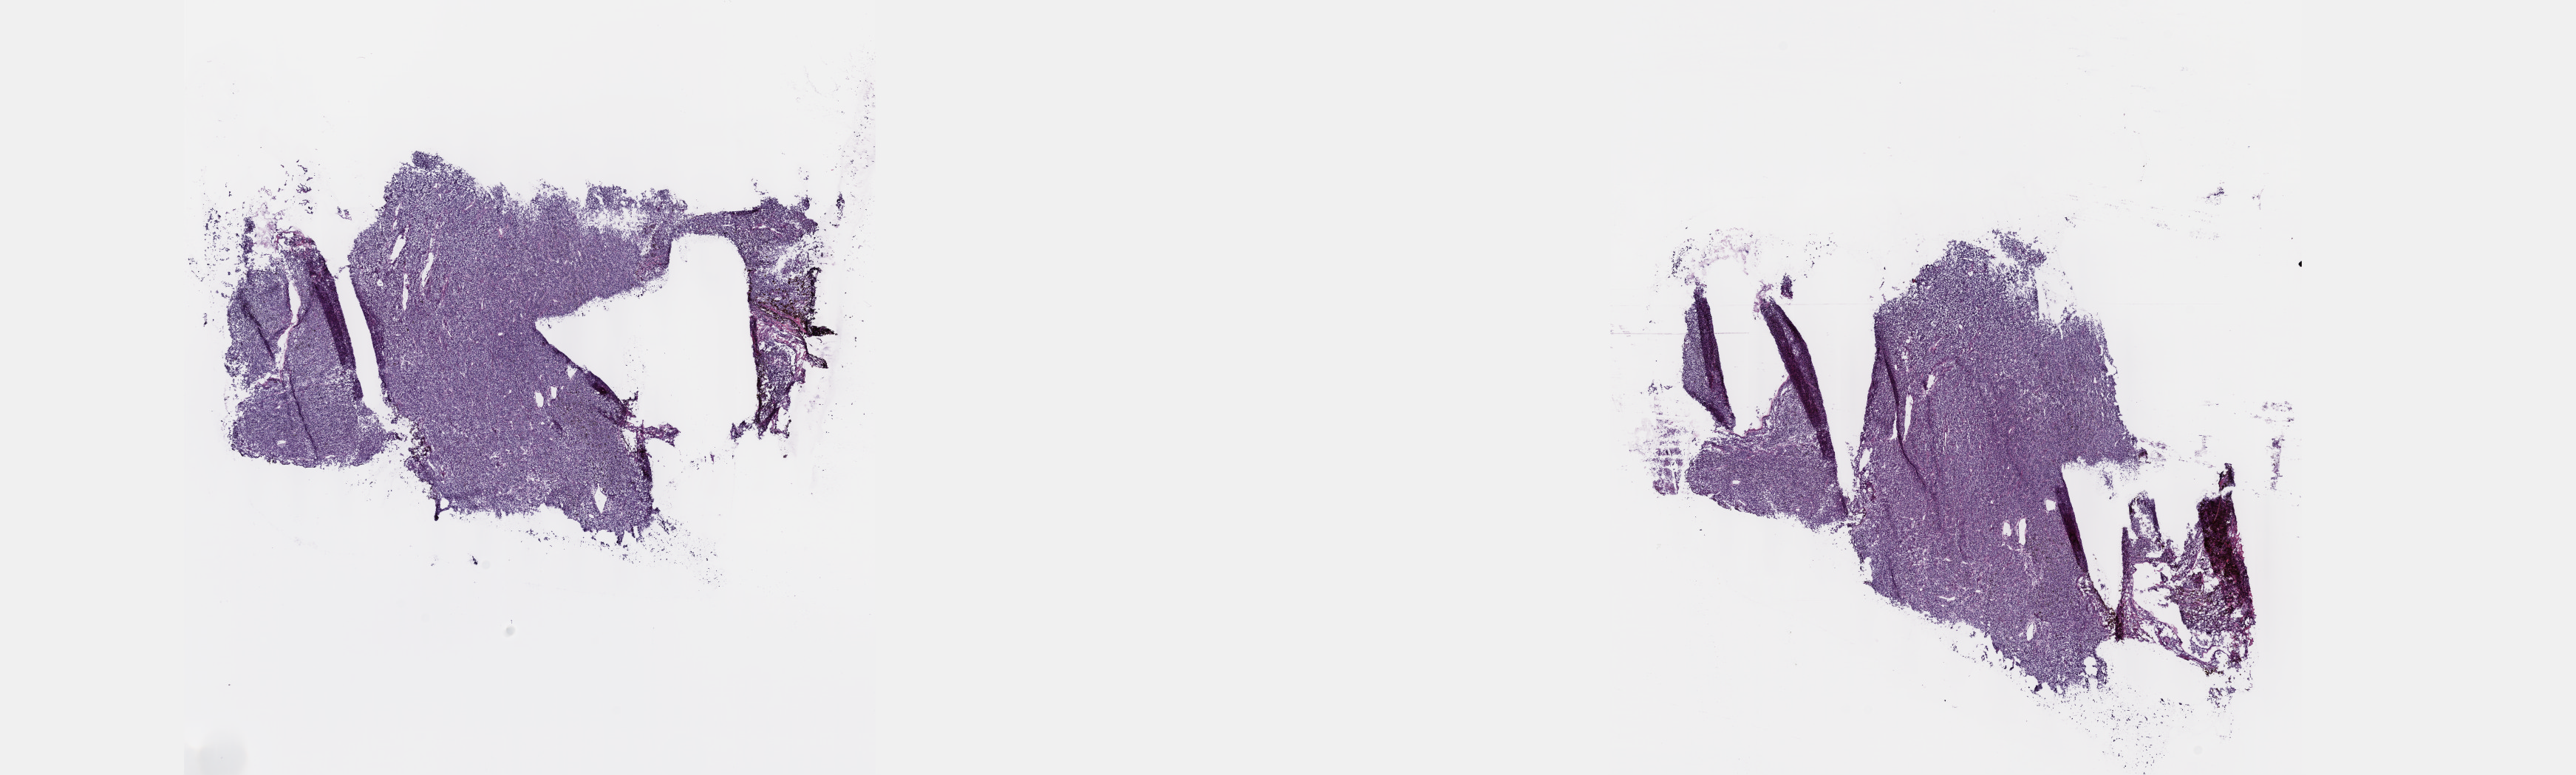
Whole-slide histology image, H&E — a low-resolution overview of the entire scanned area, about 28.2 x 8.5 mm (from a 40x scan); frozen section from the top of the tissue portion; primary tumour sample from the uvea. Male patient; age at initial diagnosis 45 years. Composition of this section per pathologist review: tumour cells 100%, tumour nuclei 80%, normal cells 0%, stromal cells 0%, necrosis 0%. Inflammatory infiltration, as recorded: lymphocyte infiltration 2%, monocyte infiltration 0%, neutrophil infiltration 0%.
AJCC pathologic stage: IIIA (7th edition). Histologic diagnosis: Spindle cell melanoma, NOS.